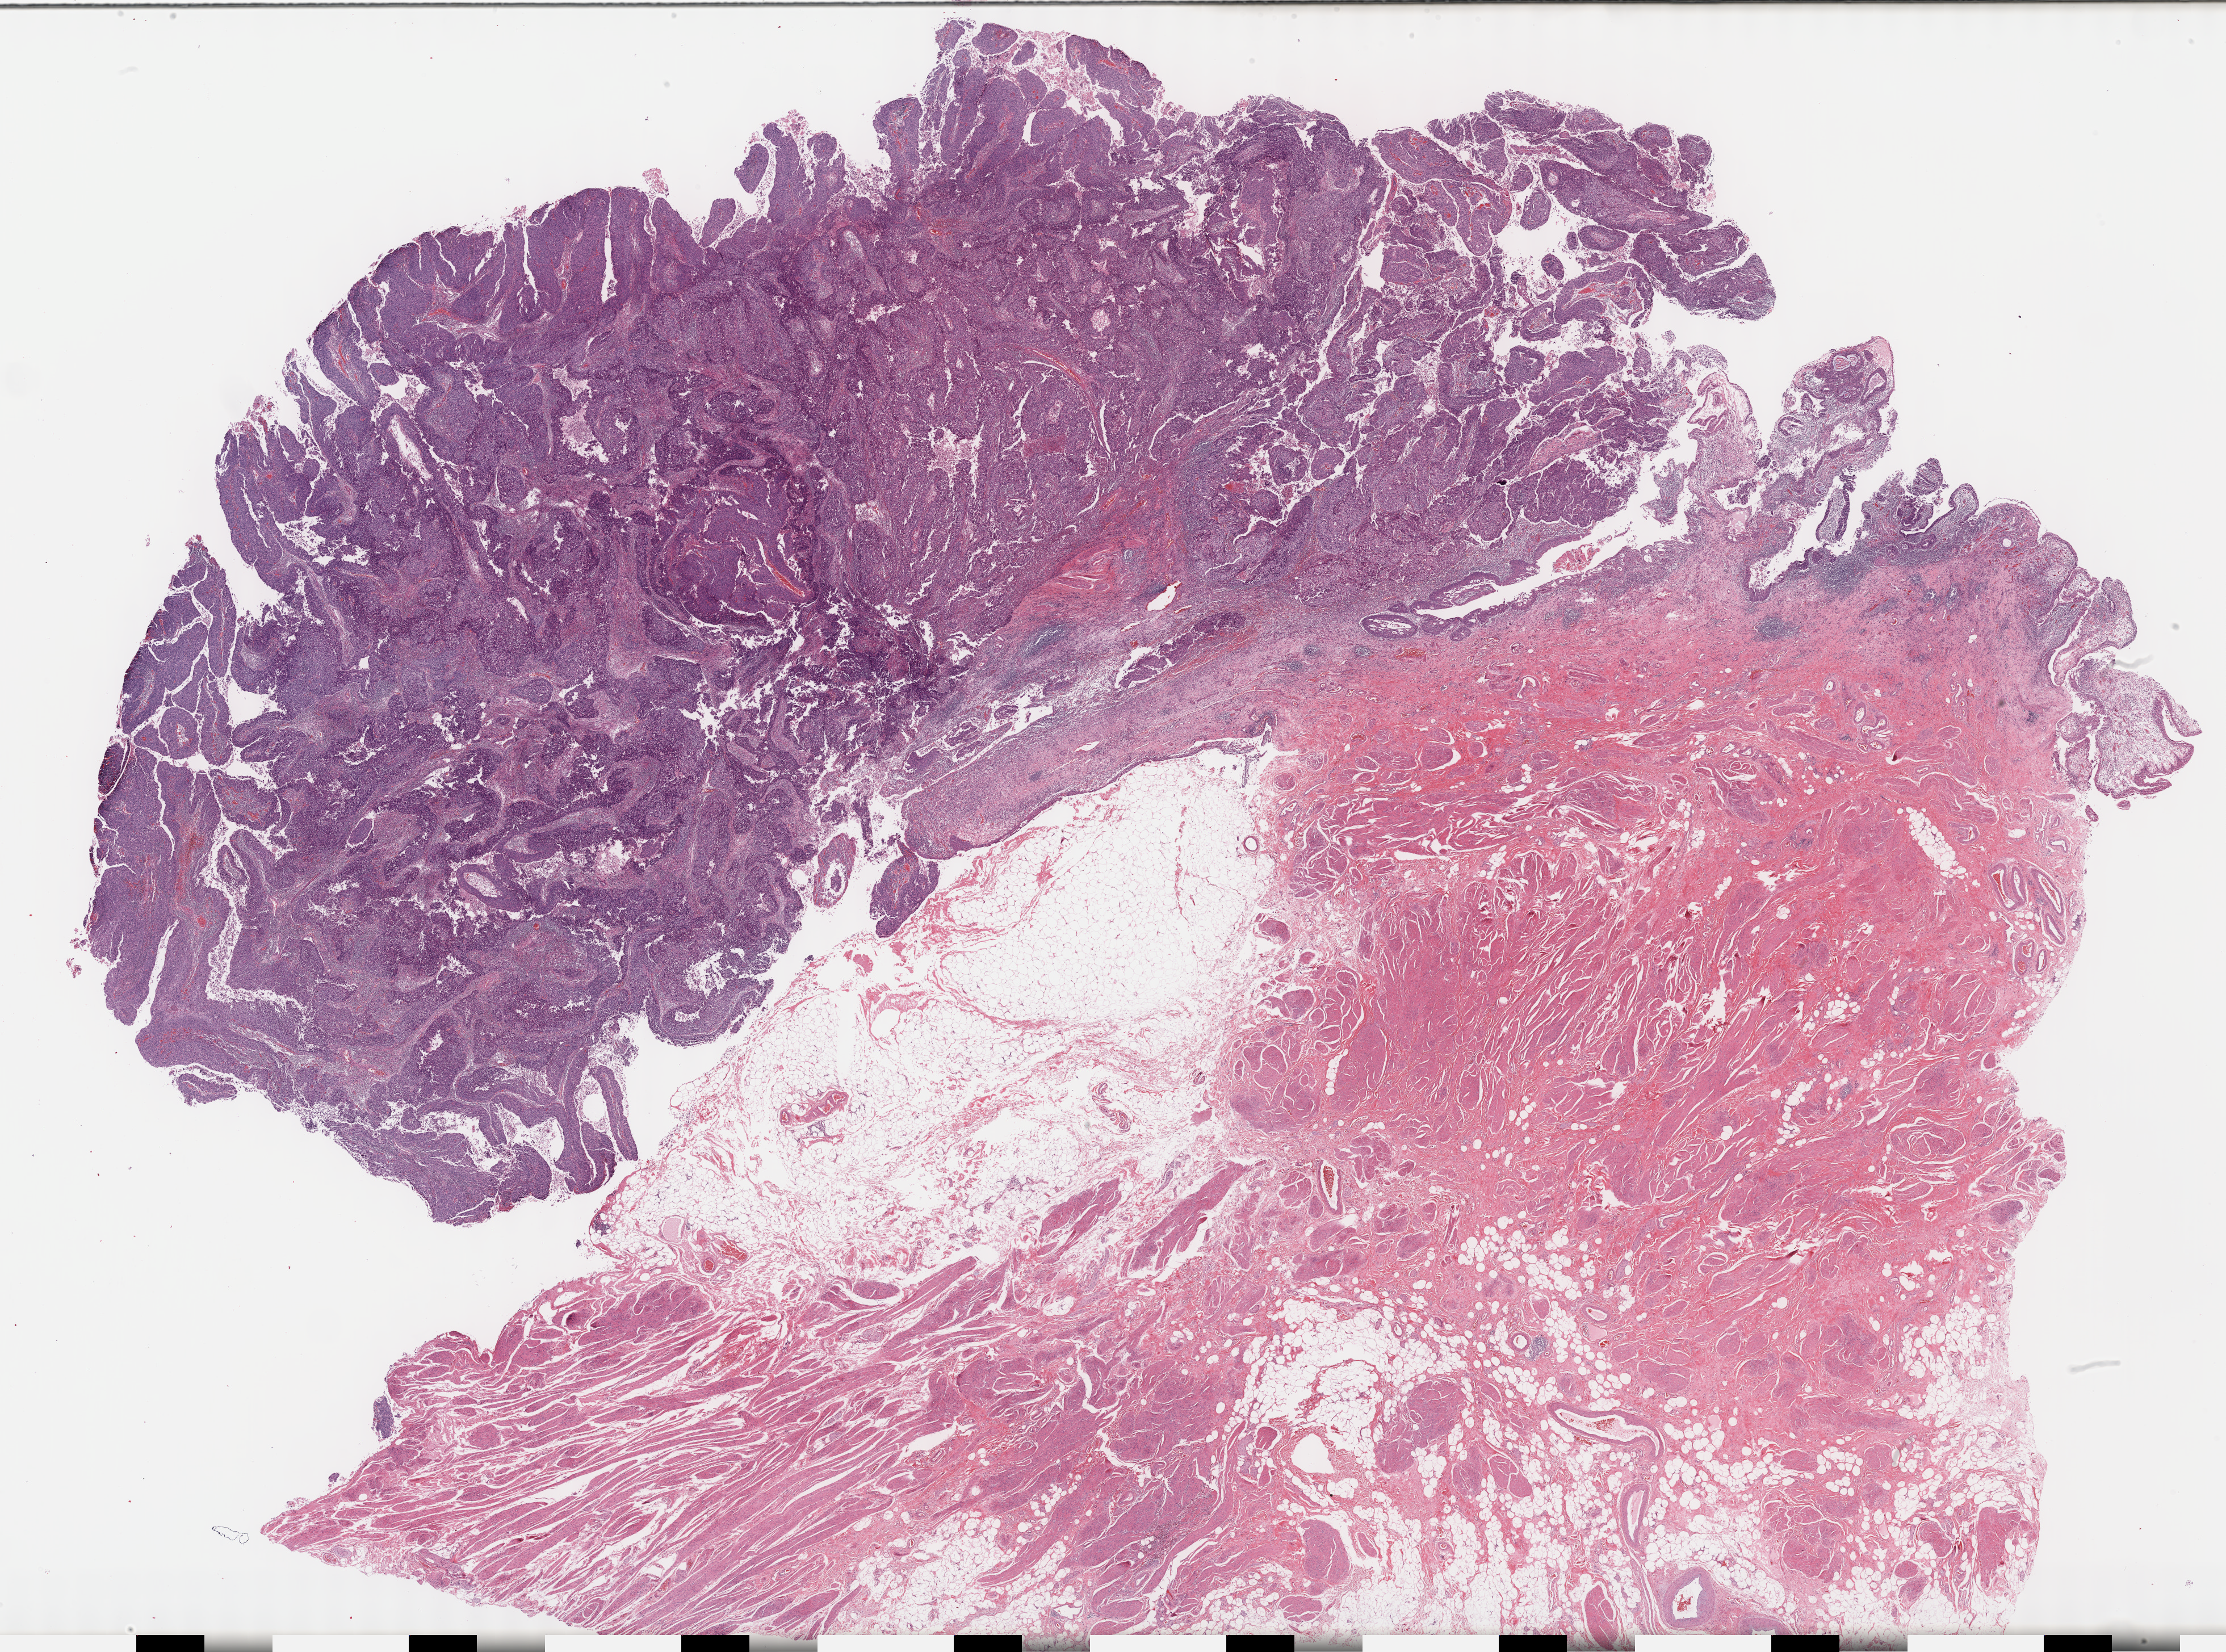
Digitized H&E tissue section (whole slide) — a low-resolution overview of the entire scanned area, about 31.7 x 23.5 mm (acquisition: 40x scan), formalin-fixed paraffin-embedded (FFPE) diagnostic section, sample: primary tumour, bladder. Male patient; age at initial diagnosis 75 years.
Pathologic diagnosis: Papillary transitional cell carcinoma (lateral wall of bladder).